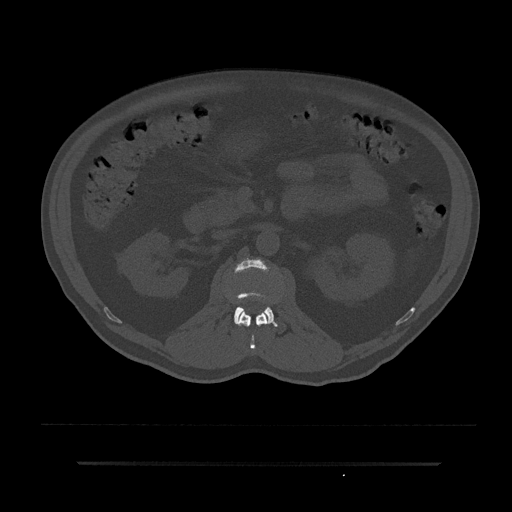
CT including the spine, one axial slice. Reconstruction kernel Br40s/3. Bone window (W 1800 / L 400 HU). 0.5 mm slice thickness. 512 × 512 image matrix. Patient: male, 59 years. Case-level facts recorded for this patient, not image findings: primary cancer: bile ducts.
Structures marked on this image (semi-automatic segmentation, software-assisted and operator-edited):
- L1 vertebra: bounding box (x1, y1, x2, y2) in pixels: (238, 310, 267, 349)
- L2 vertebra: (234, 259, 277, 326)